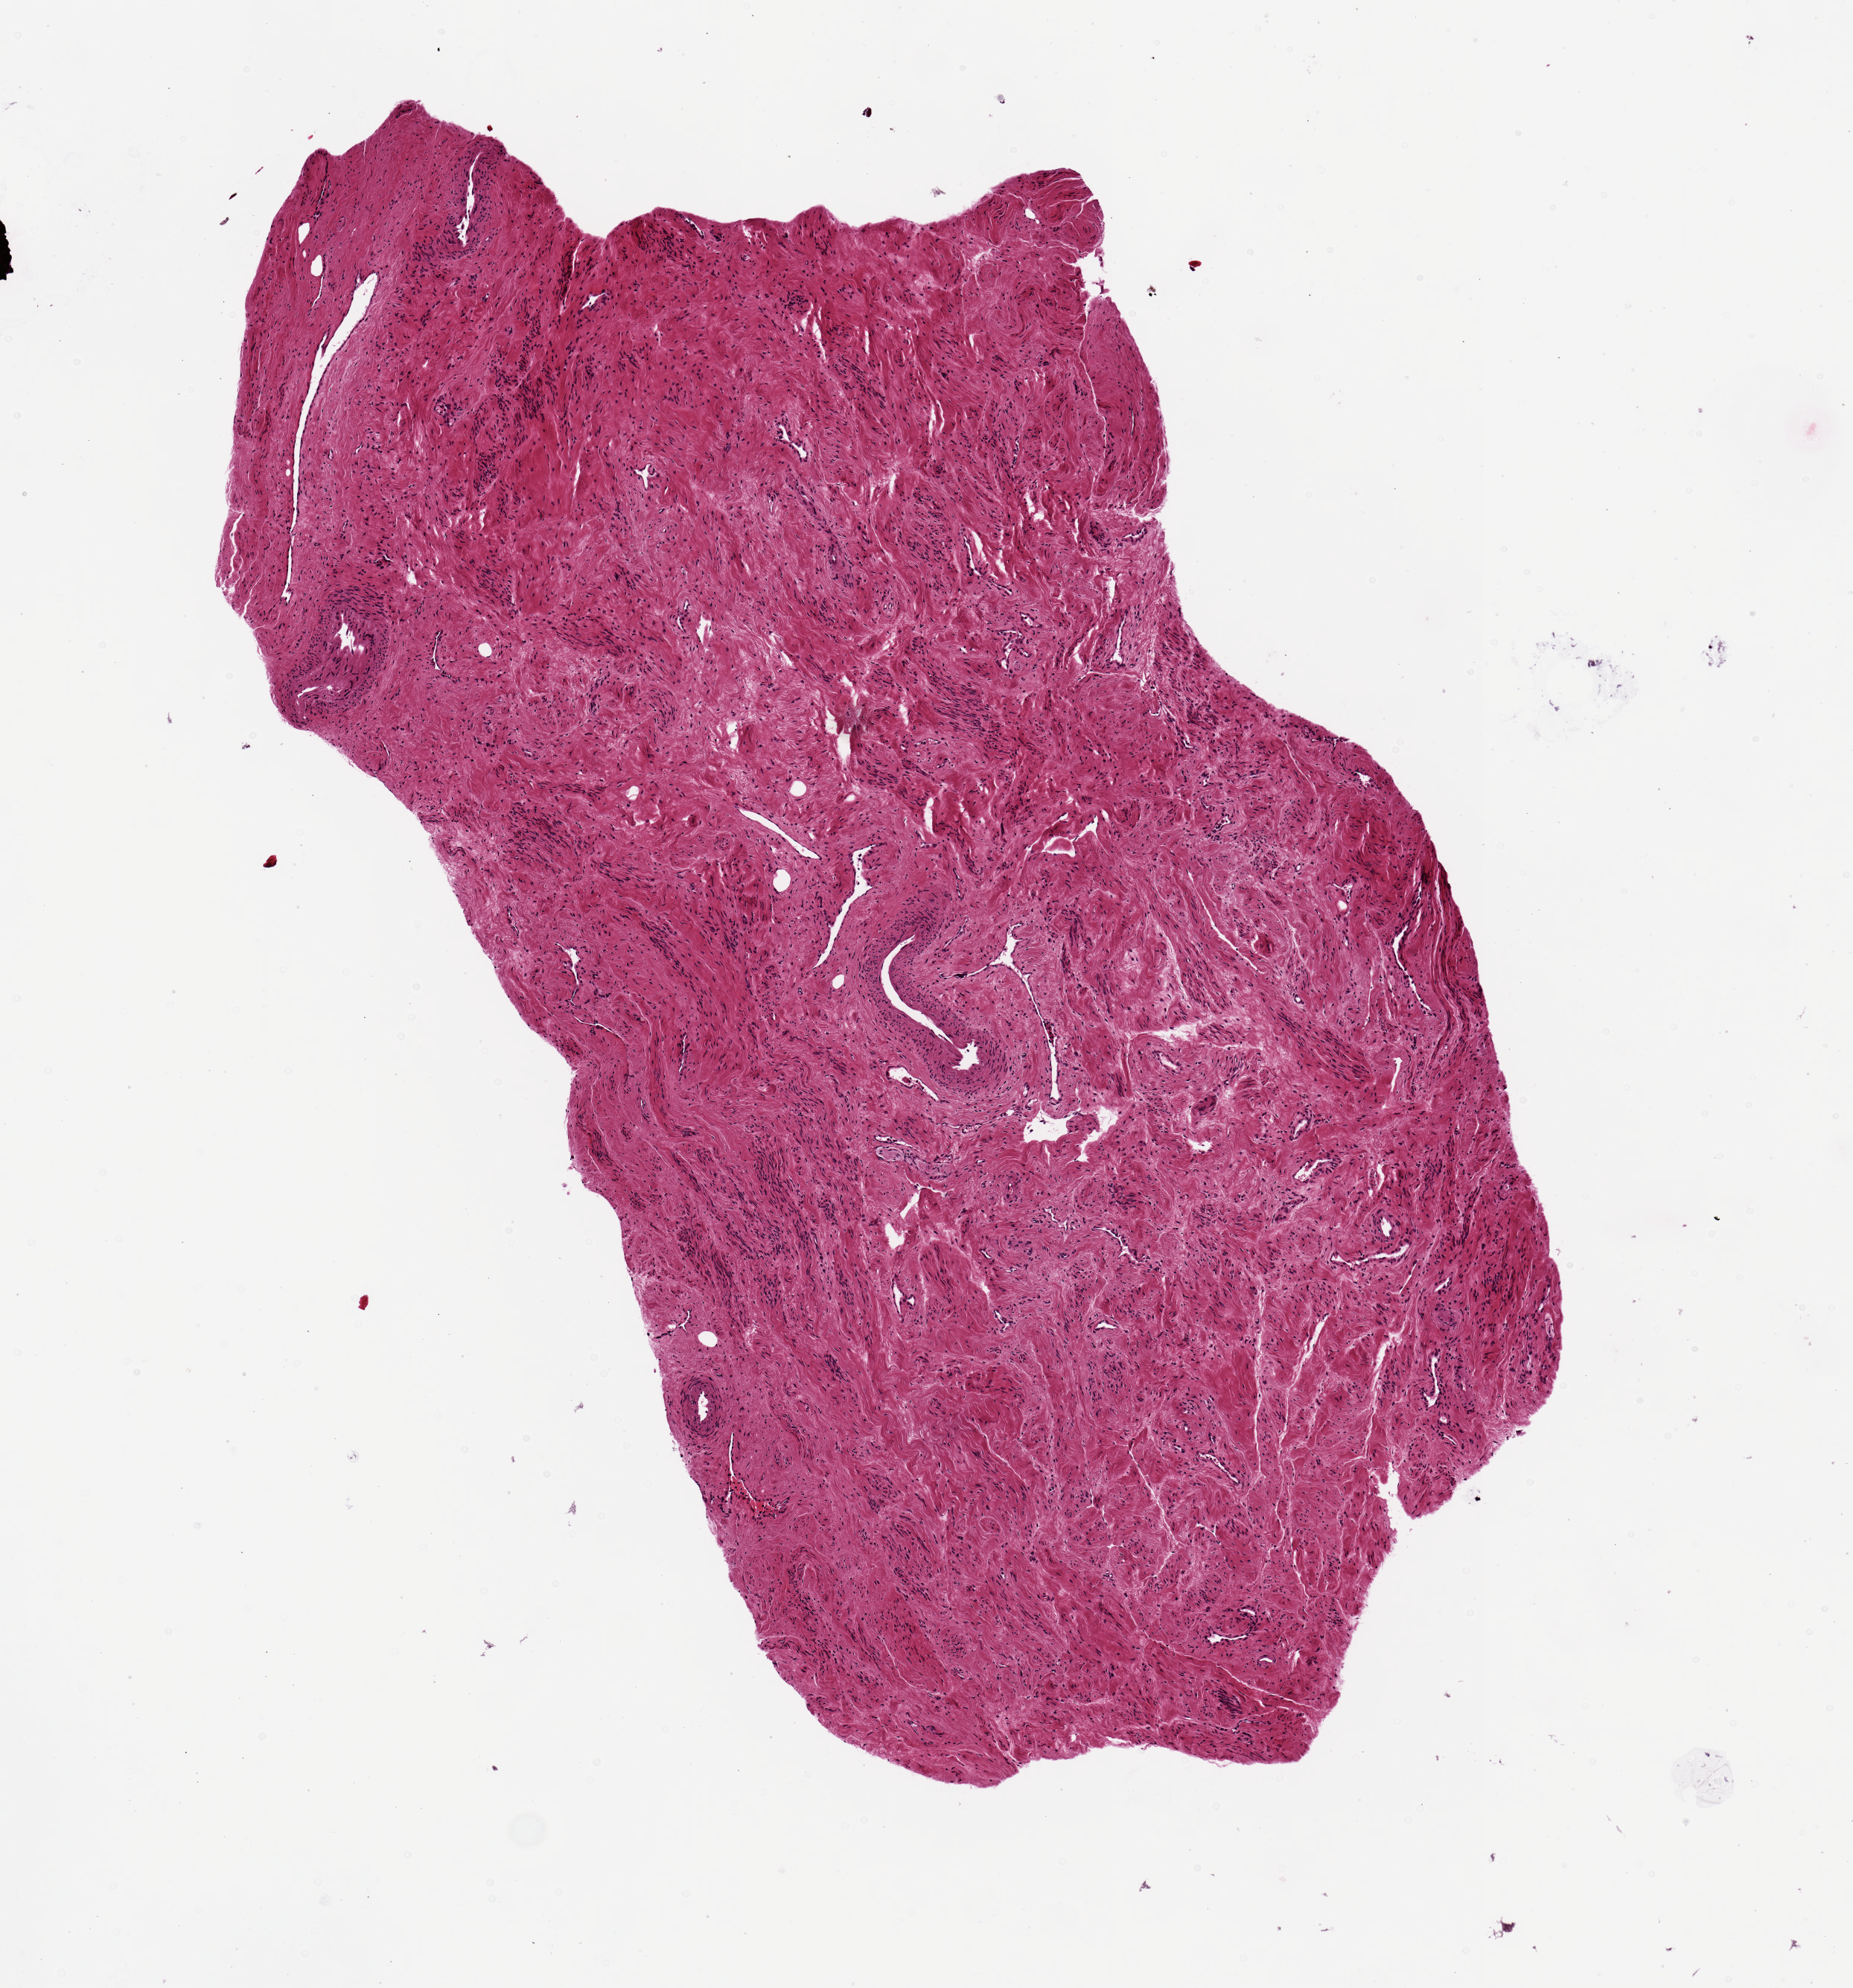
Digitized haematoxylin and eosin-stained section — whole scanned area (about 4.9 x 5.3 mm) shown as a low-resolution overview. PAXgene-fixed paraffin-embedded (PFPE) section. Sampled site (target tissue): exocervix. Donor tissue sample. Donor: female.
Reviewer comment on this tissue sample: No epithelium is present.